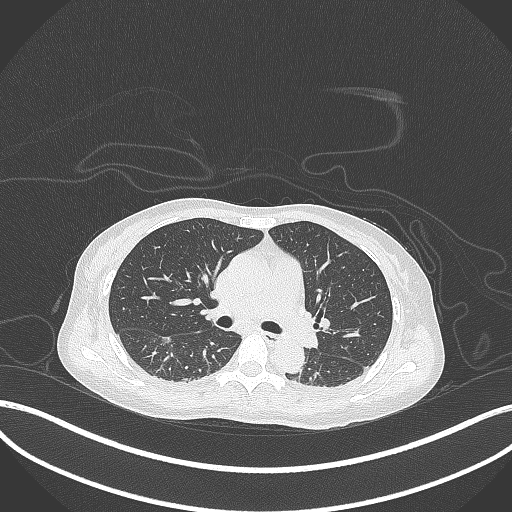
Chest CT, one axial slice. Slice 185 of 261 in the series (ordered by position). Reconstruction kernel B70f. 120 kVp. Lung window (W 1500 / L -600 HU). 512 × 512 image matrix, field of view 400 × 400 mm. Patient: female, 44 years. Case-level facts recorded for this patient, not image findings: clinical TNM (as recorded): T1c N0 M0.
Structures marked on this image (rectangle marked by the reading radiologist):
- lung tumour (recorded histology: adenocarcinoma): box from (x=158, y=335) to (x=174, y=349) px